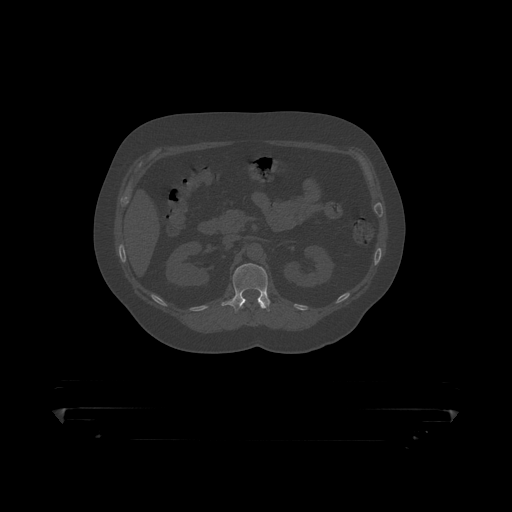
CT including the spine, one axial slice. Position 152 of 390 along the scan axis. Reconstruction kernel STANDARD. 120 kVp. Bone window (W 1800 / L 400 HU). 1.25 mm slice thickness. 512 × 512 image matrix. Male patient, age 60 years. Case-level facts recorded for this patient, not image findings: primary cancer: prostate.
Outlined on this slice (semi-automatically segmented with operator editing):
- L1 vertebra: box from (x=222, y=264) to (x=271, y=314) px
- T12 vertebra: (x=241, y=301)–(x=270, y=312)